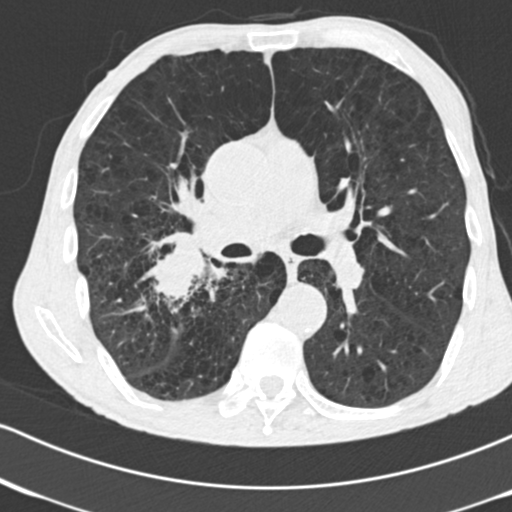
Low-dose screening chest CT, one axial slice; slice 97 of 182 in the series (ordered by position); reconstruction kernel B30f; 120 kVp; lung window (W 1500 / L -600 HU); 2 mm slice thickness; 512 × 512 image matrix.
Structures marked on this image (expert manual segmentation):
- lesion 1 (tumor, lower lobe of right lung): bounding box (x1, y1, x2, y2) in pixels: (155, 240, 209, 302)